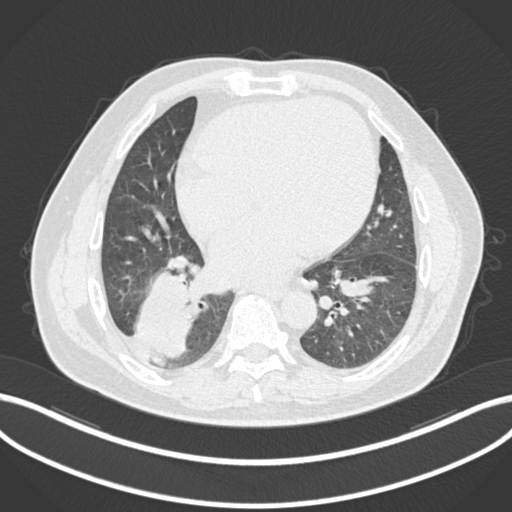
Chest CT, one axial slice. Position 63 of 200 along the scan axis. Reconstruction kernel B30f. 120 kVp. Lung window (W 1500 / L -600 HU). 1 mm slice thickness. 512 × 512 image matrix, field of view 400 × 400 mm. Patient: male, 59 years.
Outlined on this slice (bounding box drawn by a radiologist):
- lung tumour (recorded histology: adenocarcinoma): bounding box [x1, y1, x2, y2] px = [135, 270, 197, 362]